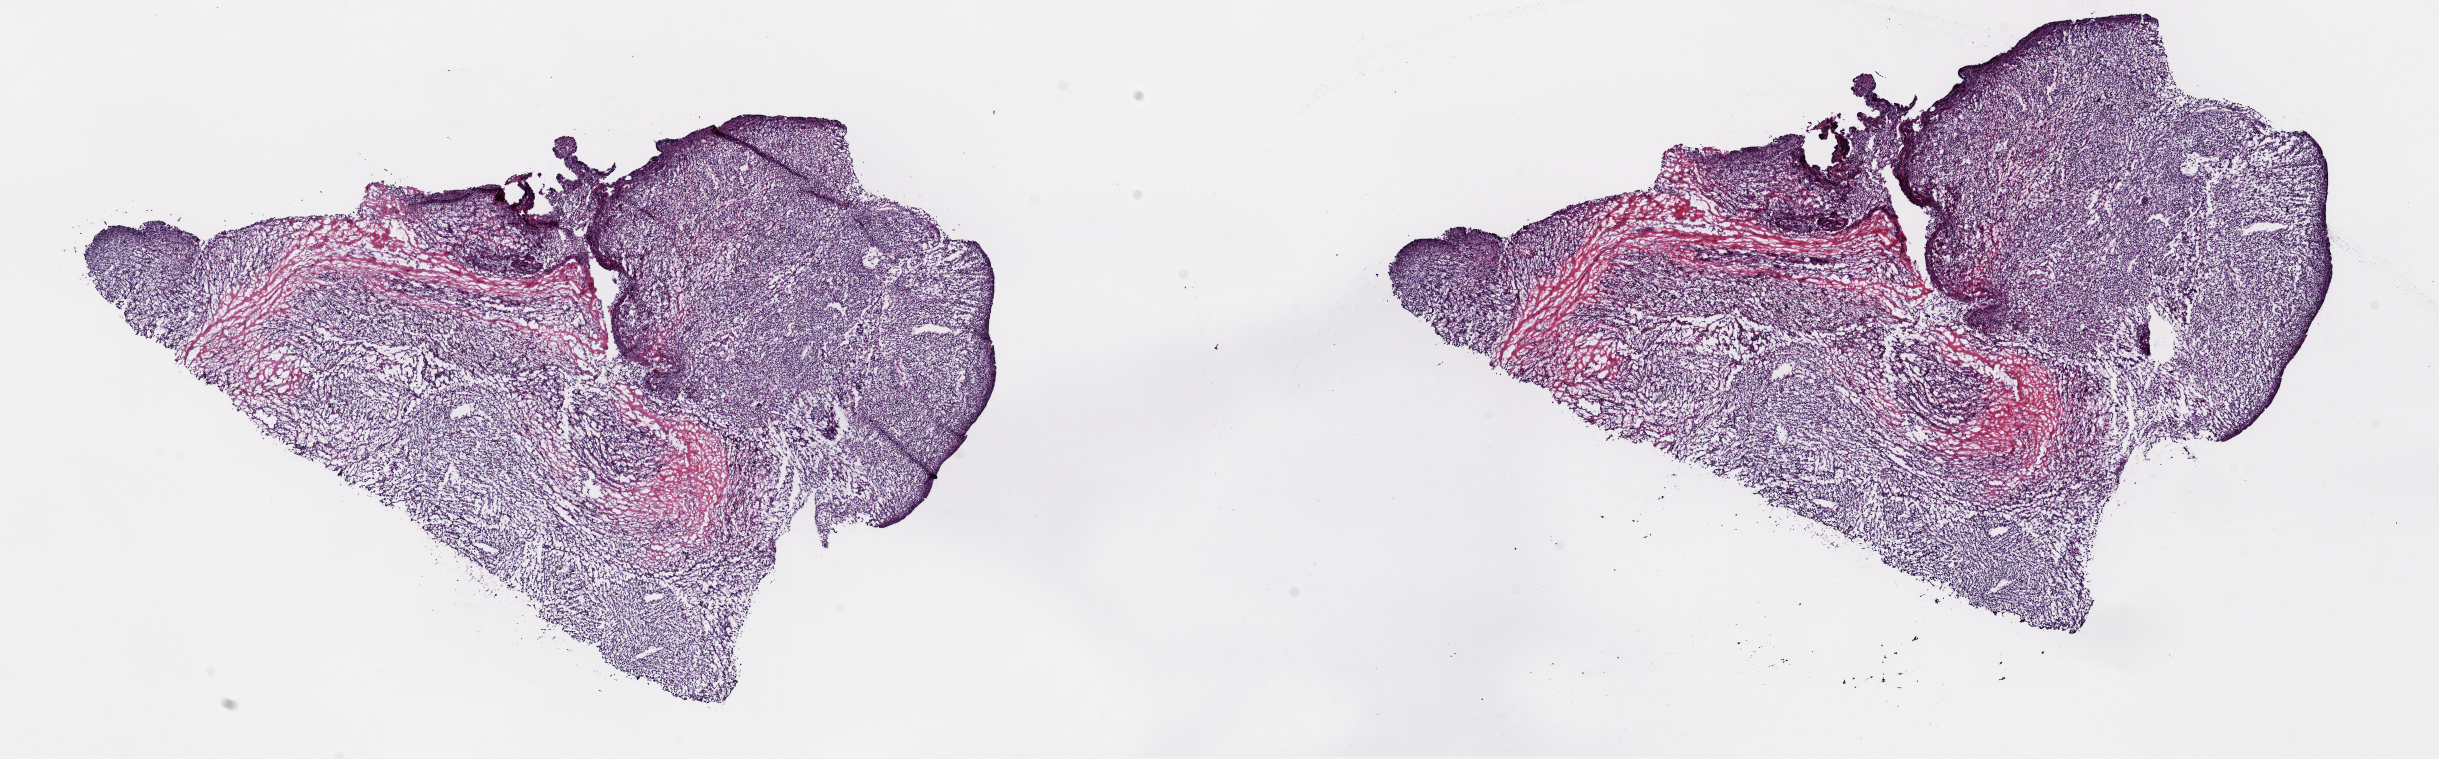
Hematoxylin and eosin (H&E) stained whole-slide image — low-resolution overview of the scanned area, about 19.3 x 6.0 mm. Frozen section. Metastatic tumour sample, sampled site: skin. Patient: male, age at initial diagnosis 71 years.
This section: metastatic tumour tissue. Patient diagnosis: Malignant melanoma, NOS.